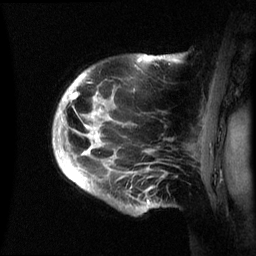
Breast MRI (dynamic contrast-enhanced), one sagittal slice. Slice 49 of 60 in the series (ordered by position). Dynamic contrast-enhanced series, image 2 of 3 at this slice position (ordered by acquisition). 1.5 T. TE 4.2 ms, TR 8.4 ms. 2.4 mm slice thickness. 256 × 256 image matrix, field of view 230 × 230 mm. Female patient, age 48 years.
Structures marked on this image (semi-automatic segmentation, software-assisted and operator-edited):
- analysis volume of interest (the breast-tissue region the enhancement analysis was run in; not a lesion): bounding box [x1, y1, x2, y2] px = [53, 55, 181, 215]
- tumour enhancement mask (voxels above the 70 % enhancement threshold inside the analysis volume of interest): [58, 87, 149, 203]